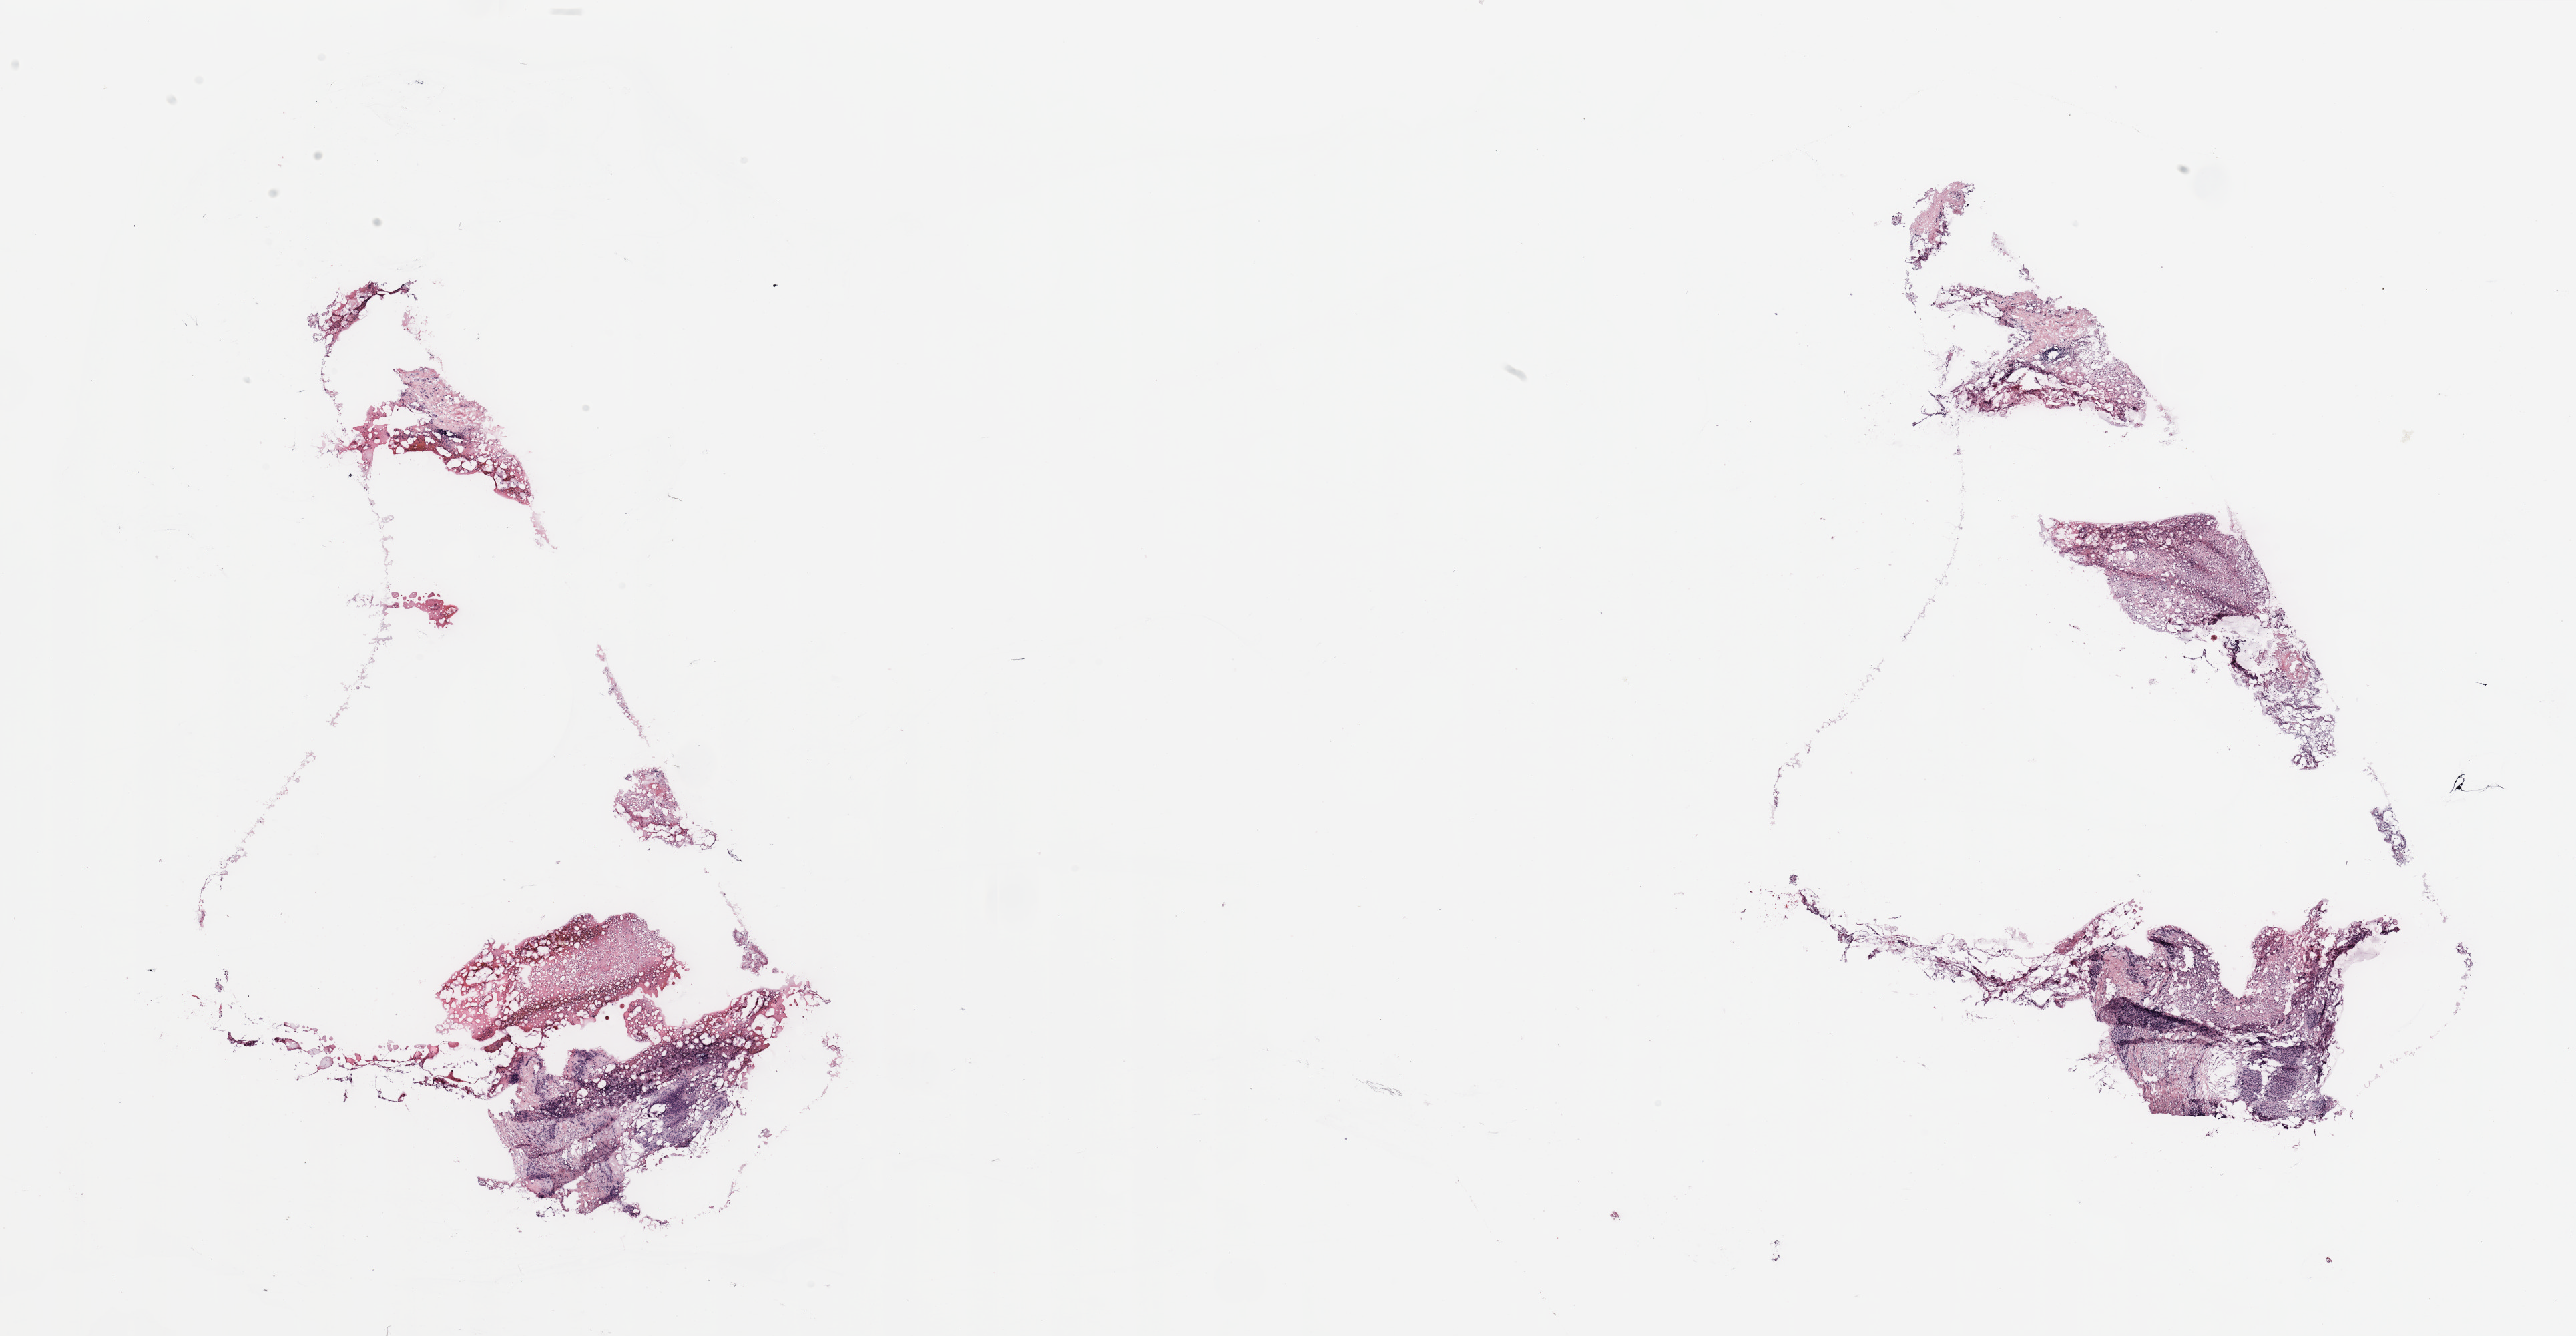
Whole-slide histology image, Hematoxylin and eosin (H&E) stained, low-resolution overview of the scanned area, about 30.5 x 15.8 mm (from a 20x scan), breast, tissue type not recorded.
Patient diagnosis (cohort enrolment): breast cancer (breast).